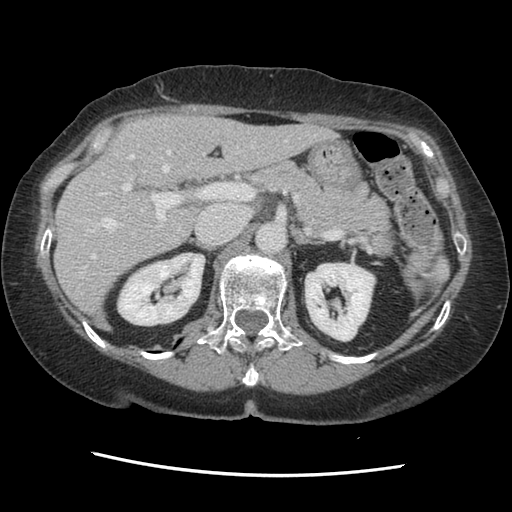
Contrast-enhanced abdominal CT, one axial slice; 120 kVp; soft-tissue window (W 400 / L 40 HU); 512 × 512 image matrix, field of view 330 × 330 mm. Female patient, age 61 years. From the clinical record (not read from this slice): diagnosis: colorectal cancer liver metastases, imaged before liver resection.
Annotated regions visible in this slice (expert manual segmentation):
- hepatic veins: bounding box [x1, y1, x2, y2] px = [82, 140, 287, 272]
- liver: [56, 115, 330, 313]
- planned liver remnant (the part of the liver to remain after resection): [56, 115, 330, 313]
- portal vein (with intrahepatic branches): [101, 154, 247, 227]